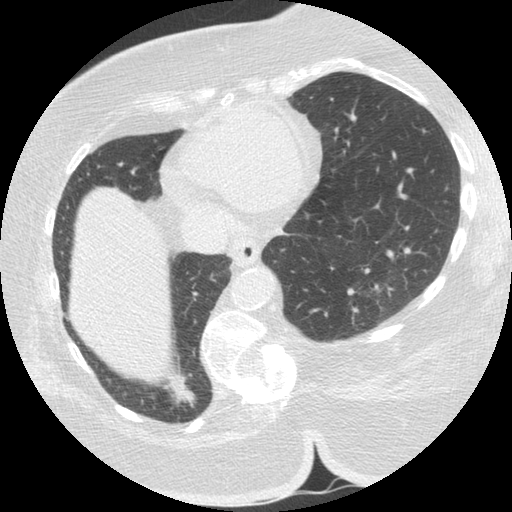
Low-dose screening chest CT, one axial slice. Slice 49 of 151 in the series (ordered by position). Reconstruction kernel STANDARD. 140 kVp. Lung window (W 1500 / L -600 HU). 512 × 512 image matrix, field of view 340 × 340 mm.
Outlined on this slice (manually delineated by an expert):
- lesion 1 (tumor, lower lobe of right lung): box from (x=164, y=372) to (x=196, y=406) px